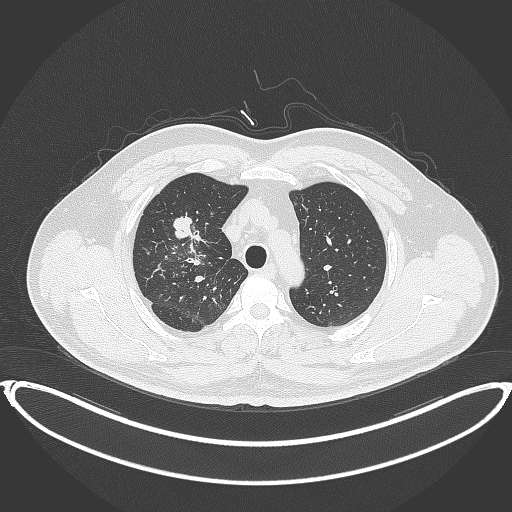
Chest CT, one axial slice. Slice 301 of 399 in the series (ordered by position). Reconstruction kernel B70f. 120 kVp. Lung window (W 1500 / L -600 HU). 1 mm slice thickness. 512 × 512 image matrix. Male patient, age 53 years. Case-level facts recorded for this patient, not image findings: clinical TNM (as recorded): T2a N0 M0.
Outlined on this slice (bounding box drawn by a radiologist):
- lung tumour (recorded histology: adenocarcinoma): bounding box (x1, y1, x2, y2) in pixels: (169, 211, 201, 248)